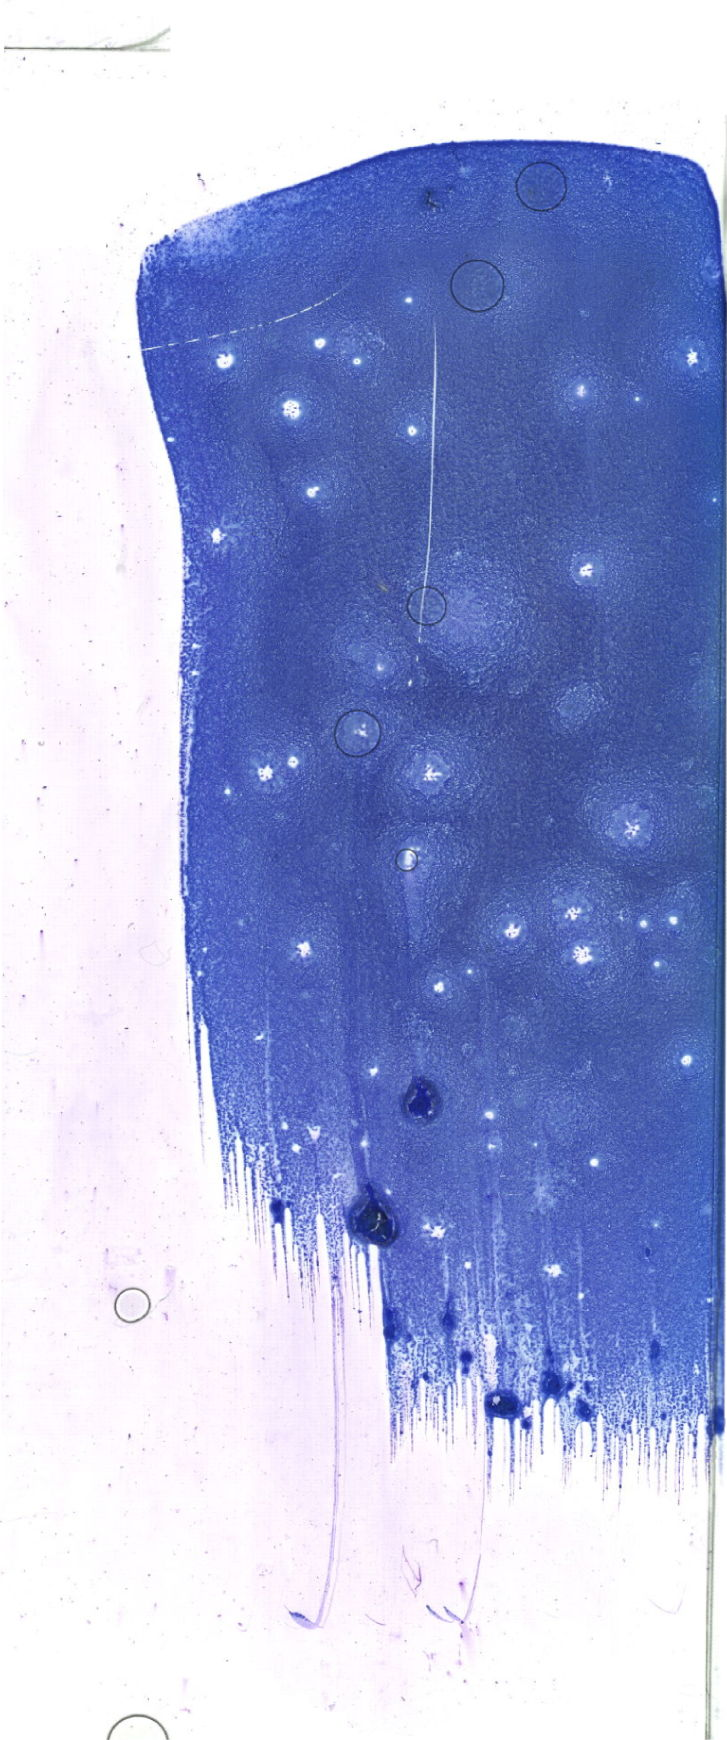
May-Grünwald-Giemsa (MGG)-stained marrow aspirate smear (whole slide) — low-resolution overview of the scanned area, about 20.6 x 49.3 mm. Female patient.
Diagnosis: Acute Myeloid Leukemia with Maturation.